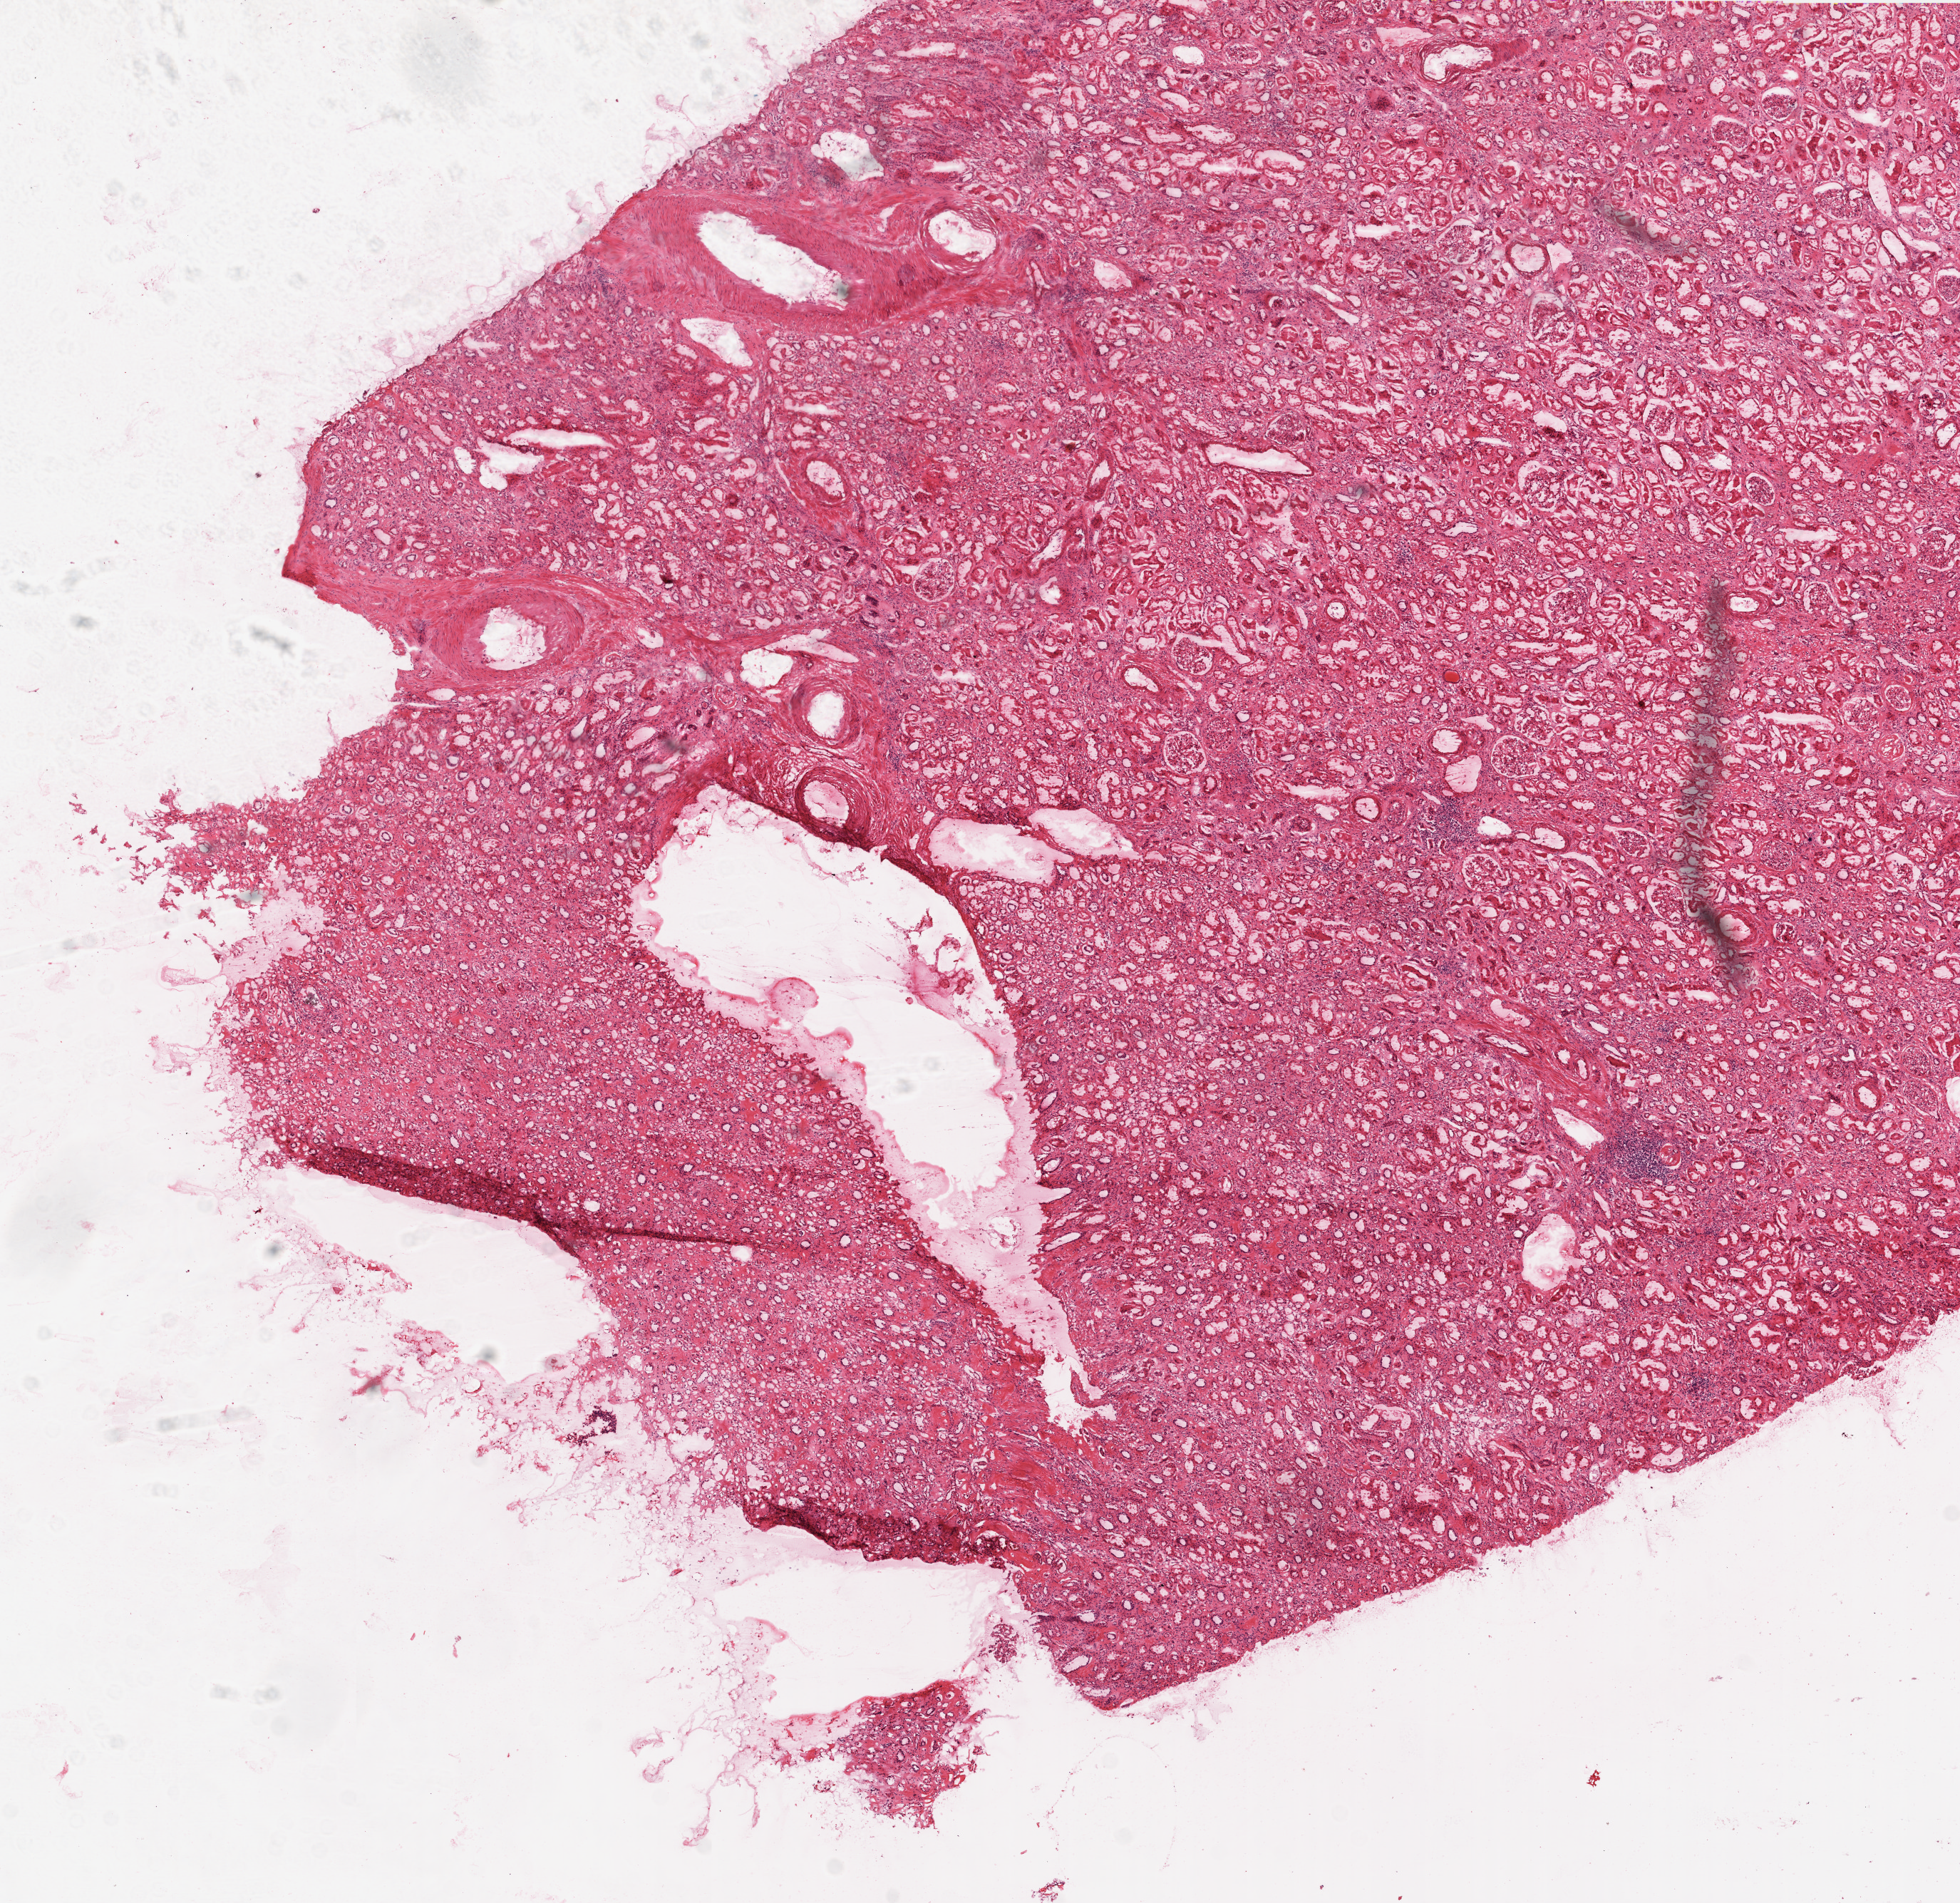
Digitized Hematoxylin and eosin (H&E) stained tissue section (whole slide) — a low-resolution overview of the entire scanned area, about 11.0 x 10.7 mm, frozen section from the top of the tissue portion, solid tissue normal (non-tumour tissue) sample from the kidney. Male, age 62 years at initial diagnosis.
This section: solid tissue normal (non-tumour) sample from the same patient. Patient diagnosis: Clear cell adenocarcinoma, NOS.